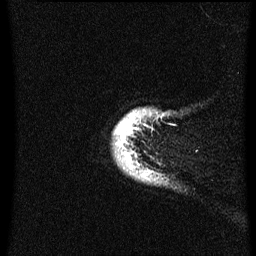
Breast MRI (dynamic contrast-enhanced), one sagittal slice. Slice 58 of 60 in the series (ordered by position). Dynamic contrast-enhanced series, image 2 of 3 at this slice position (ordered by acquisition). 1.5 T. TE 4.2 ms, TR 8.4 ms. 2.3 mm slice thickness. 256 × 256 image matrix, field of view 200 × 200 mm. Female patient, age 38 years. From the clinical record (not read from this slice): setting: breast cancer imaged before/during neoadjuvant chemotherapy; receptor status: HER2-positive.
Outlined on this slice (semi-automatic segmentation, software-assisted and operator-edited):
- analysis volume of interest (the breast-tissue region the enhancement analysis was run in; not a lesion): box from (x=114, y=108) to (x=167, y=183) px
- tumour enhancement mask (voxels above the 70 % enhancement threshold inside the analysis volume of interest): (x=118, y=120)–(x=131, y=163)